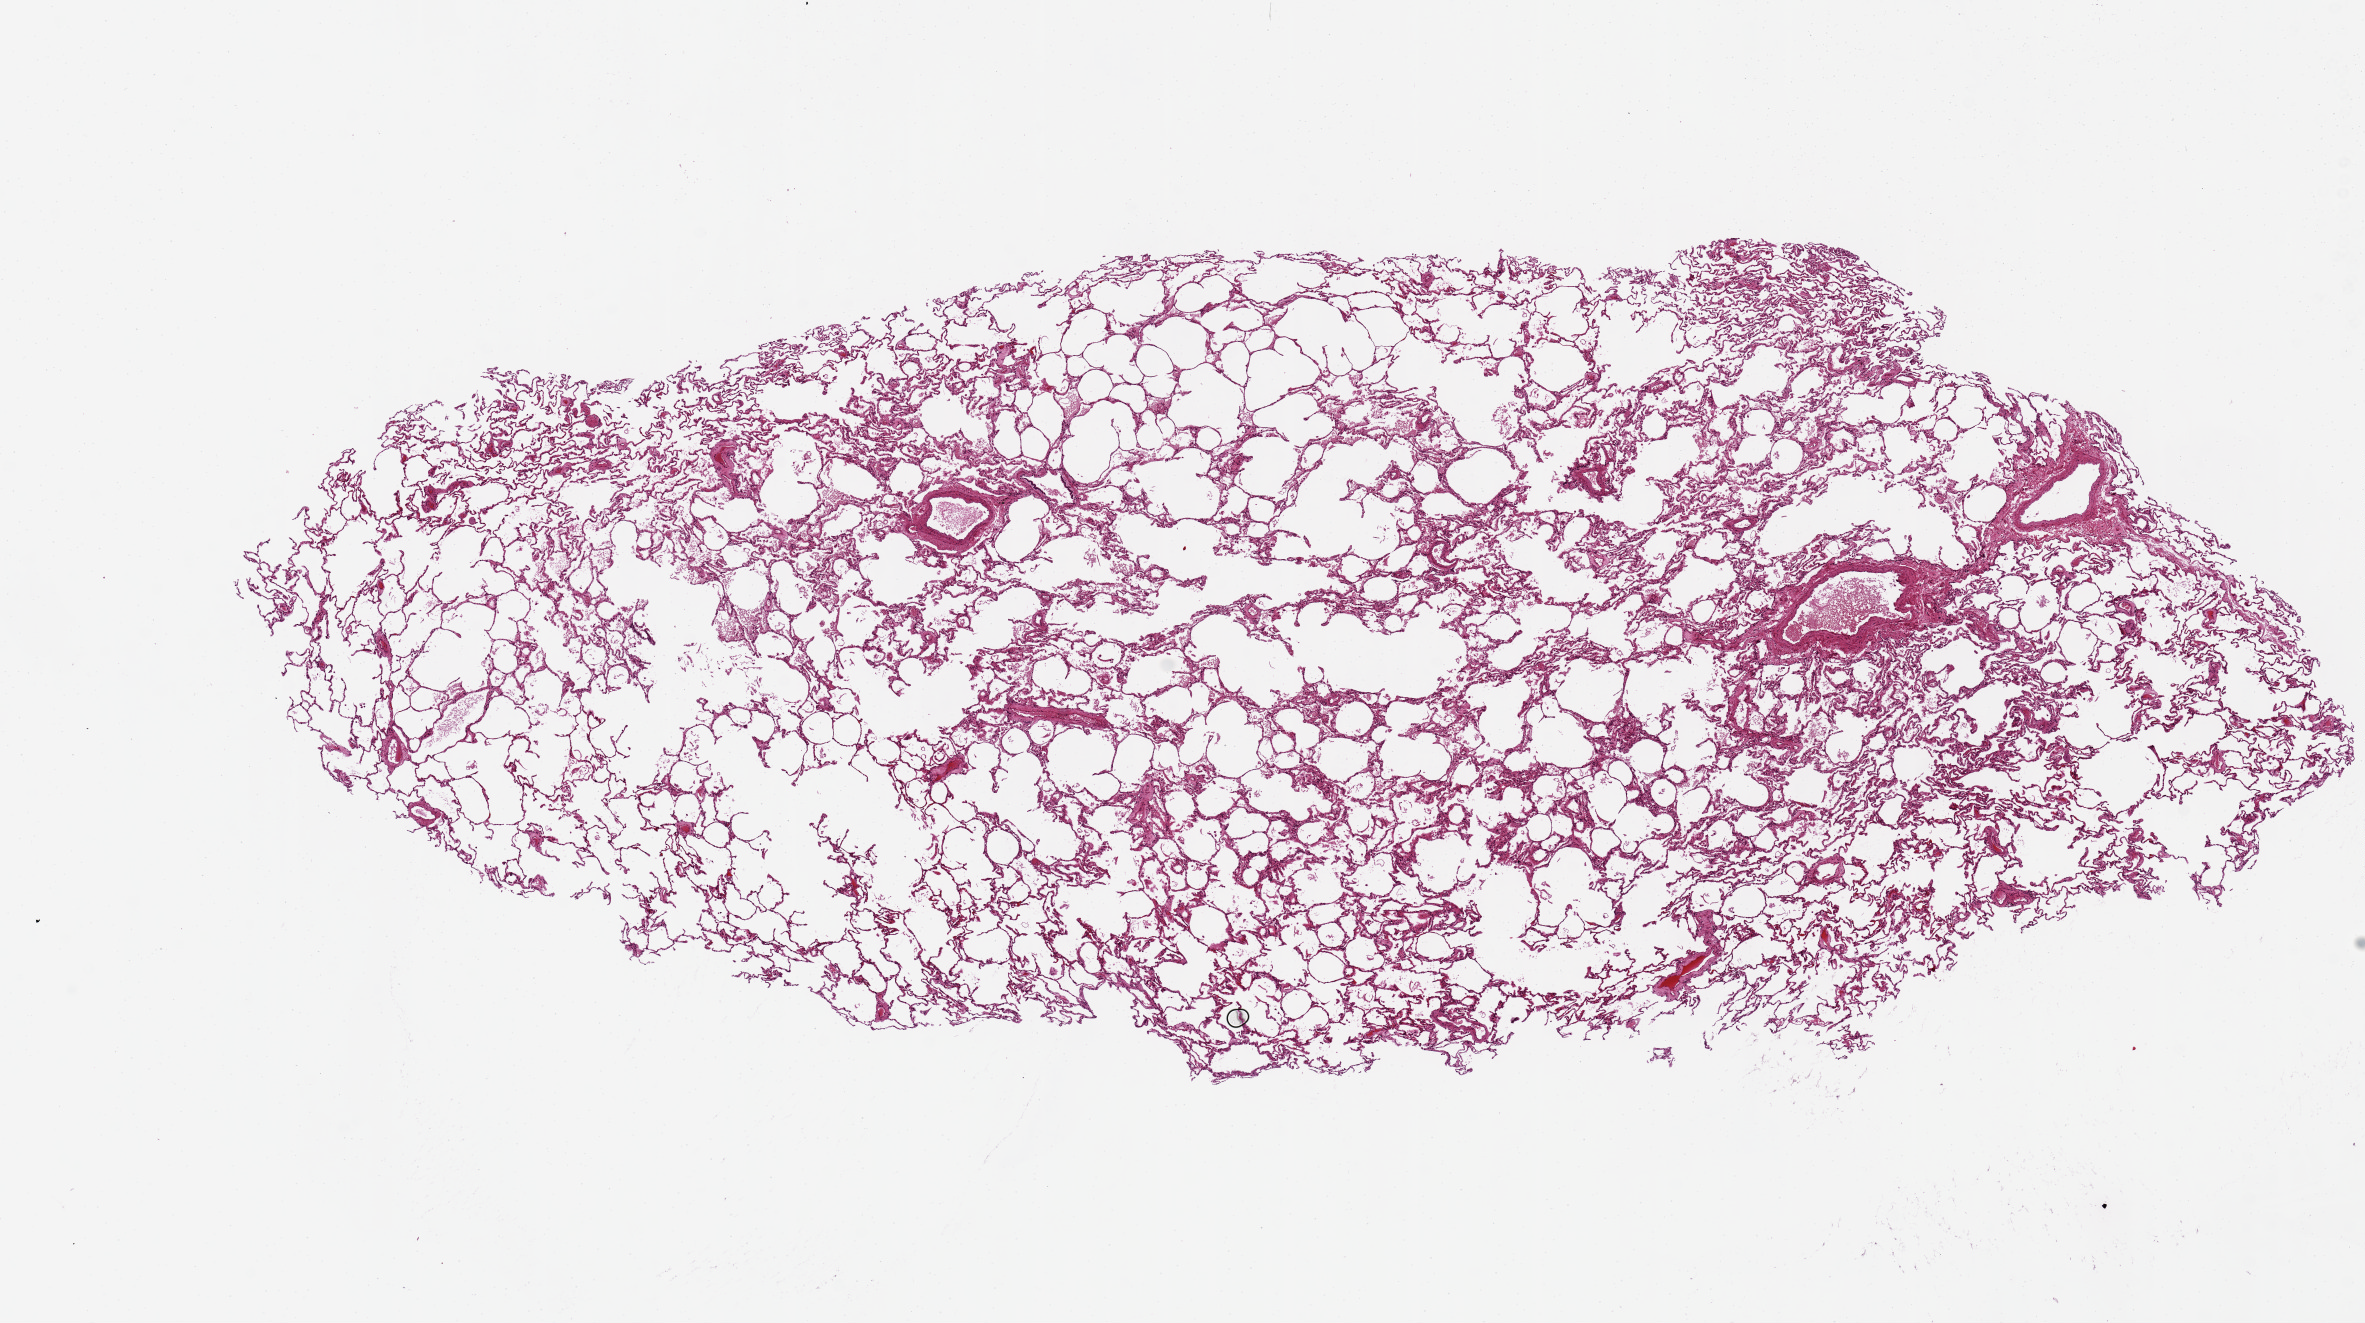
Whole-slide image, H&E stain — a low-resolution overview of the entire scanned area, about 18.7 x 10.5 mm, PAXgene-fixed, paraffin-embedded tissue, sampled site (target tissue): lung, donor tissue sample.
Reviewer comment on this tissue sample: 16x6 mm; mild edema.